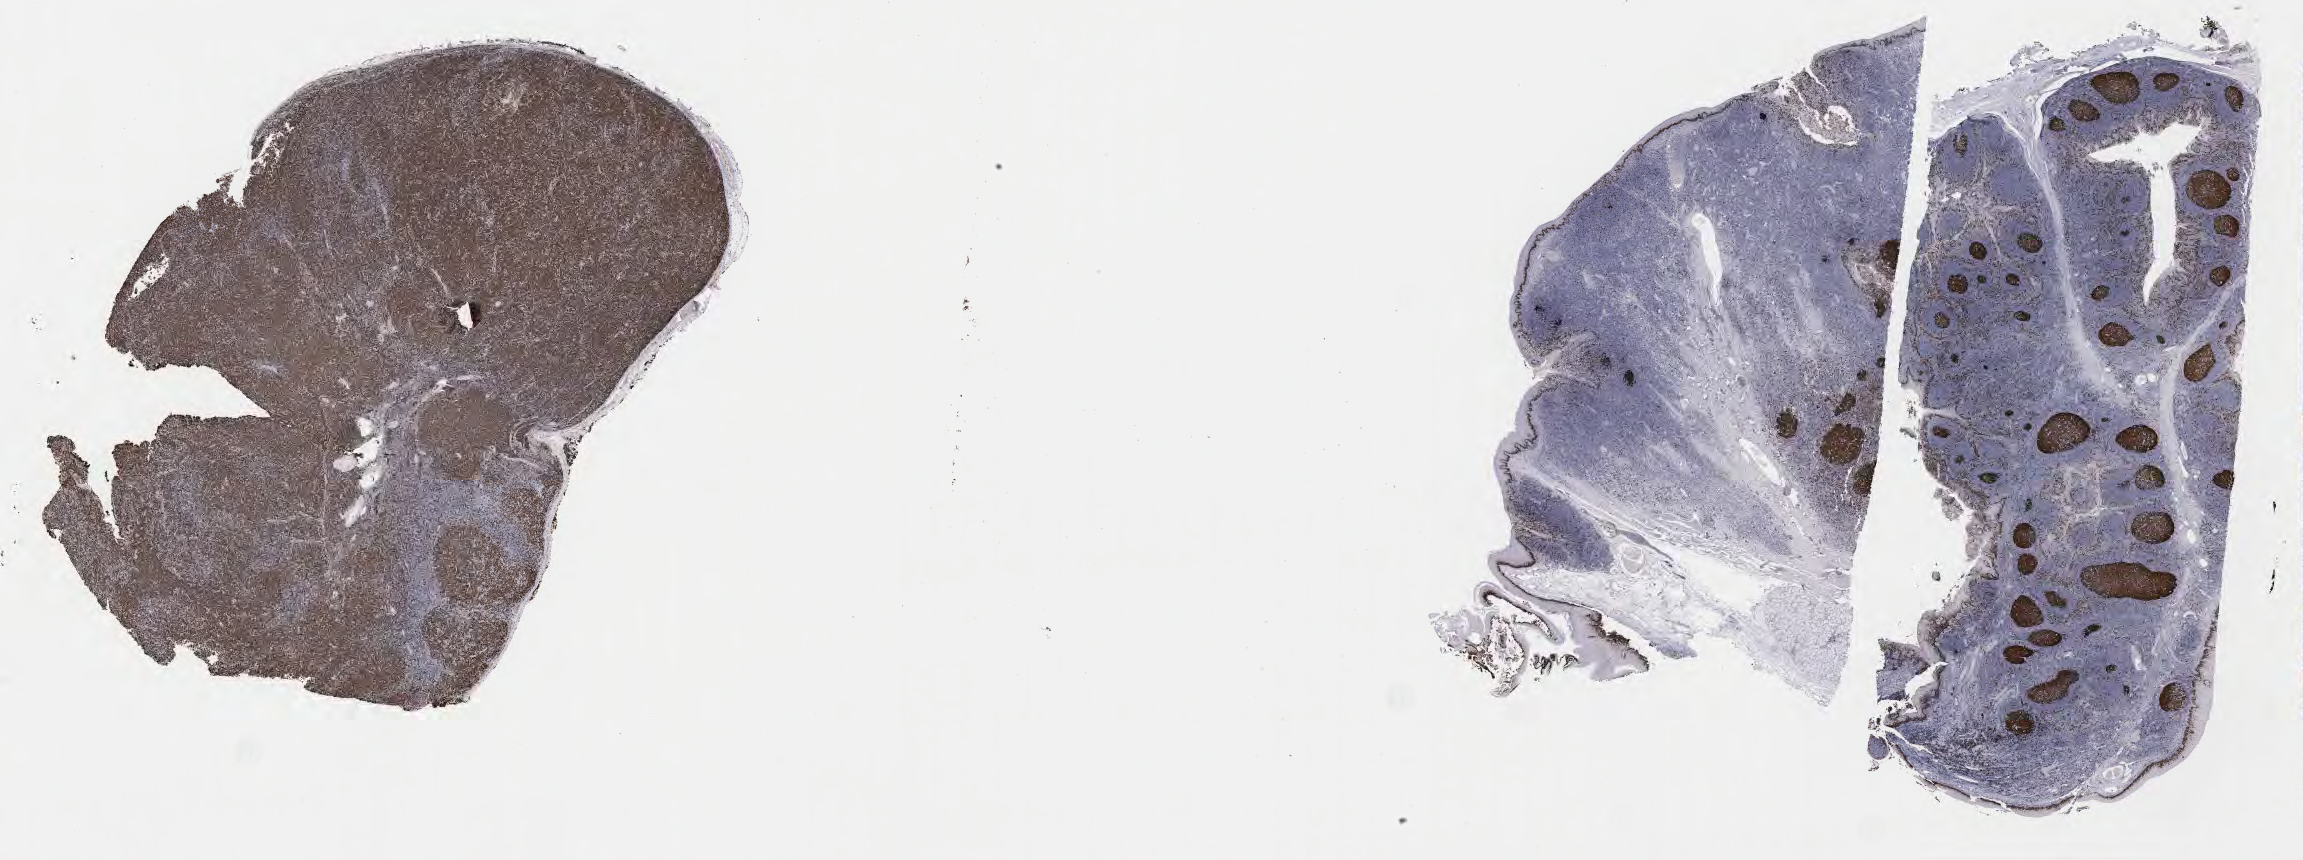
Immunohistochemistry (IHC) whole-slide image stained for Ki-67 — low-resolution overview of the scanned area, about 37.2 x 13.9 mm, tumor tissue, anatomic site: lymph node. Patient male; 32 years old.
Diagnosis: Diffuse large B-cell lymphoma, NOS.